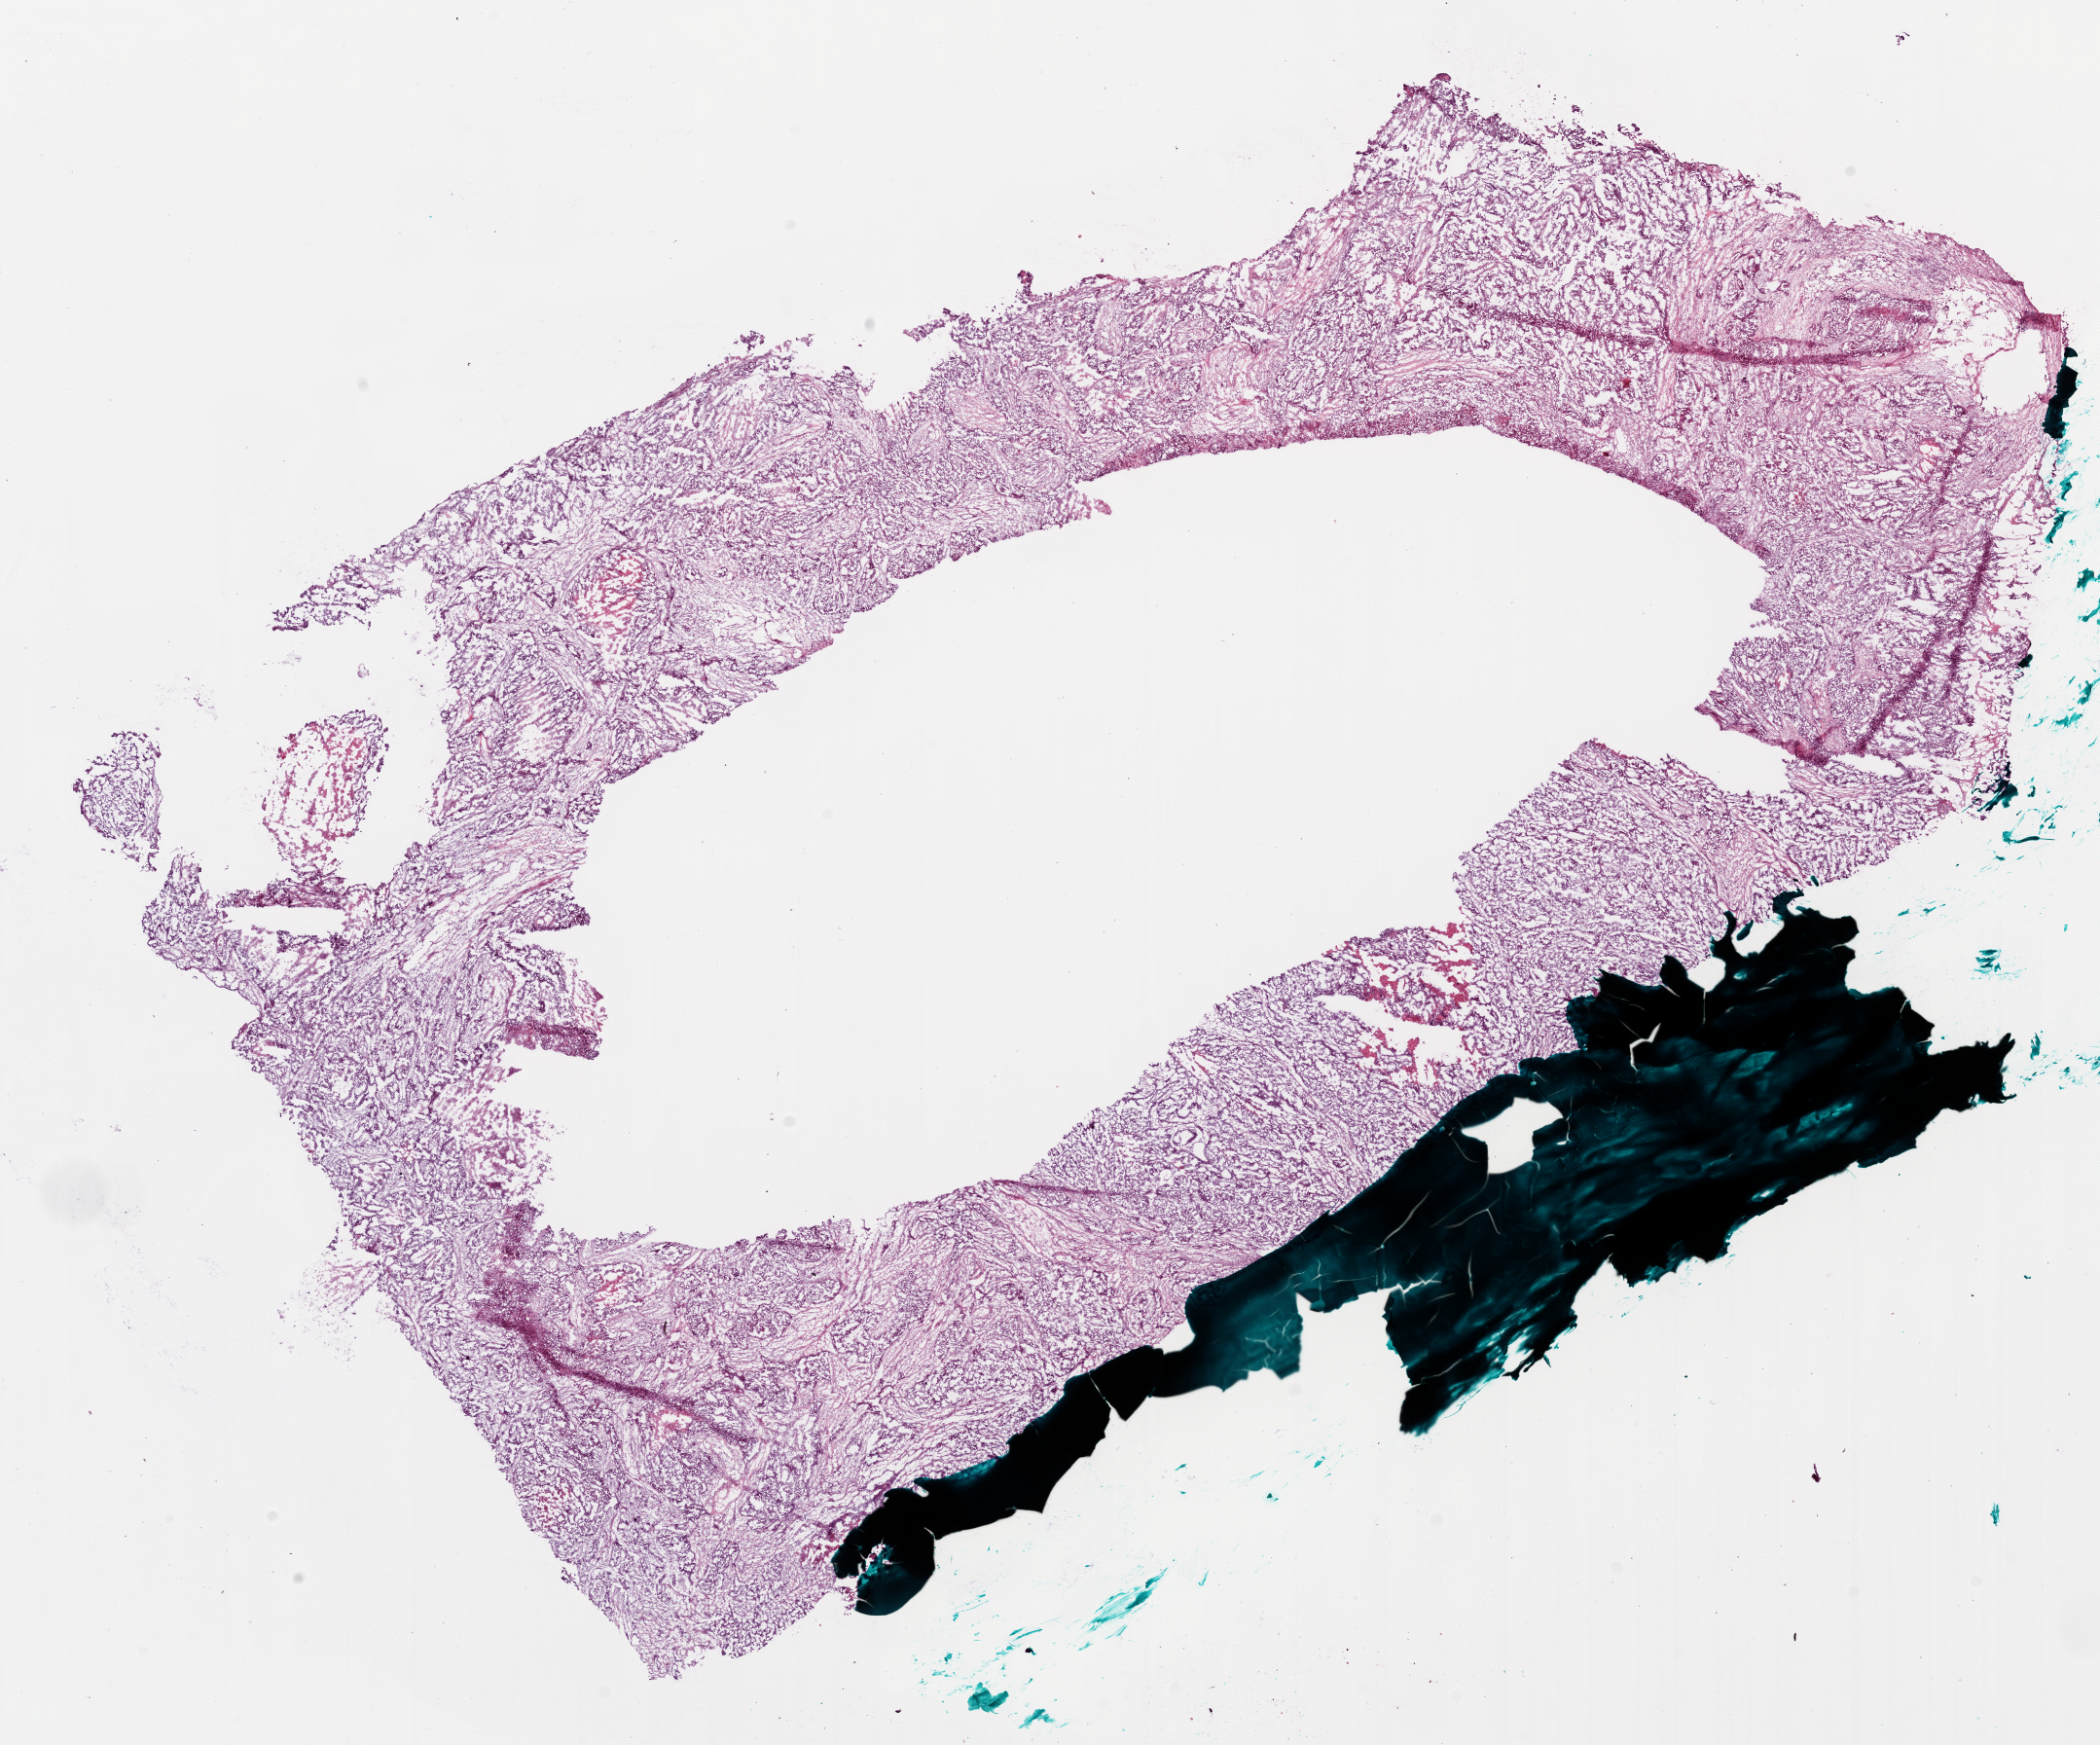
Digitized H&E-stained tissue section (whole slide), a low-resolution overview of the entire scanned area, about 17.4 x 14.5 mm (slide scanned at 20x); frozen section; sample: primary tumour, ovary. Female patient; age at initial diagnosis 42 years. Histologic grade: G3 (poorly differentiated). Pathologist review of this section (percent, as recorded): tumour cells 75%, tumour nuclei 80%, normal cells 20%, necrosis 5%.
Pathologic diagnosis: Serous cystadenocarcinoma, NOS. FIGO stage: IIIC.